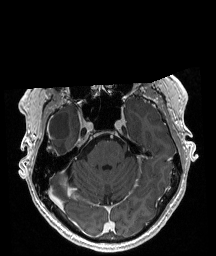
Brain MRI from a brain-tumour surgery series, one axial slice. Position 137 of 208 along the scan axis. T1-weighted post-contrast. 1 mm slice thickness. 216 × 256 image matrix, field of view 211 × 250 mm. Case-level facts recorded for this patient, not image findings: histopathology: Astrocytoma; WHO grade: 4; IDH mutation: yes.
Outlined on this slice (outlined manually by an expert reader):
- tumour: bounding box [x1, y1, x2, y2] px = [46, 144, 57, 155]